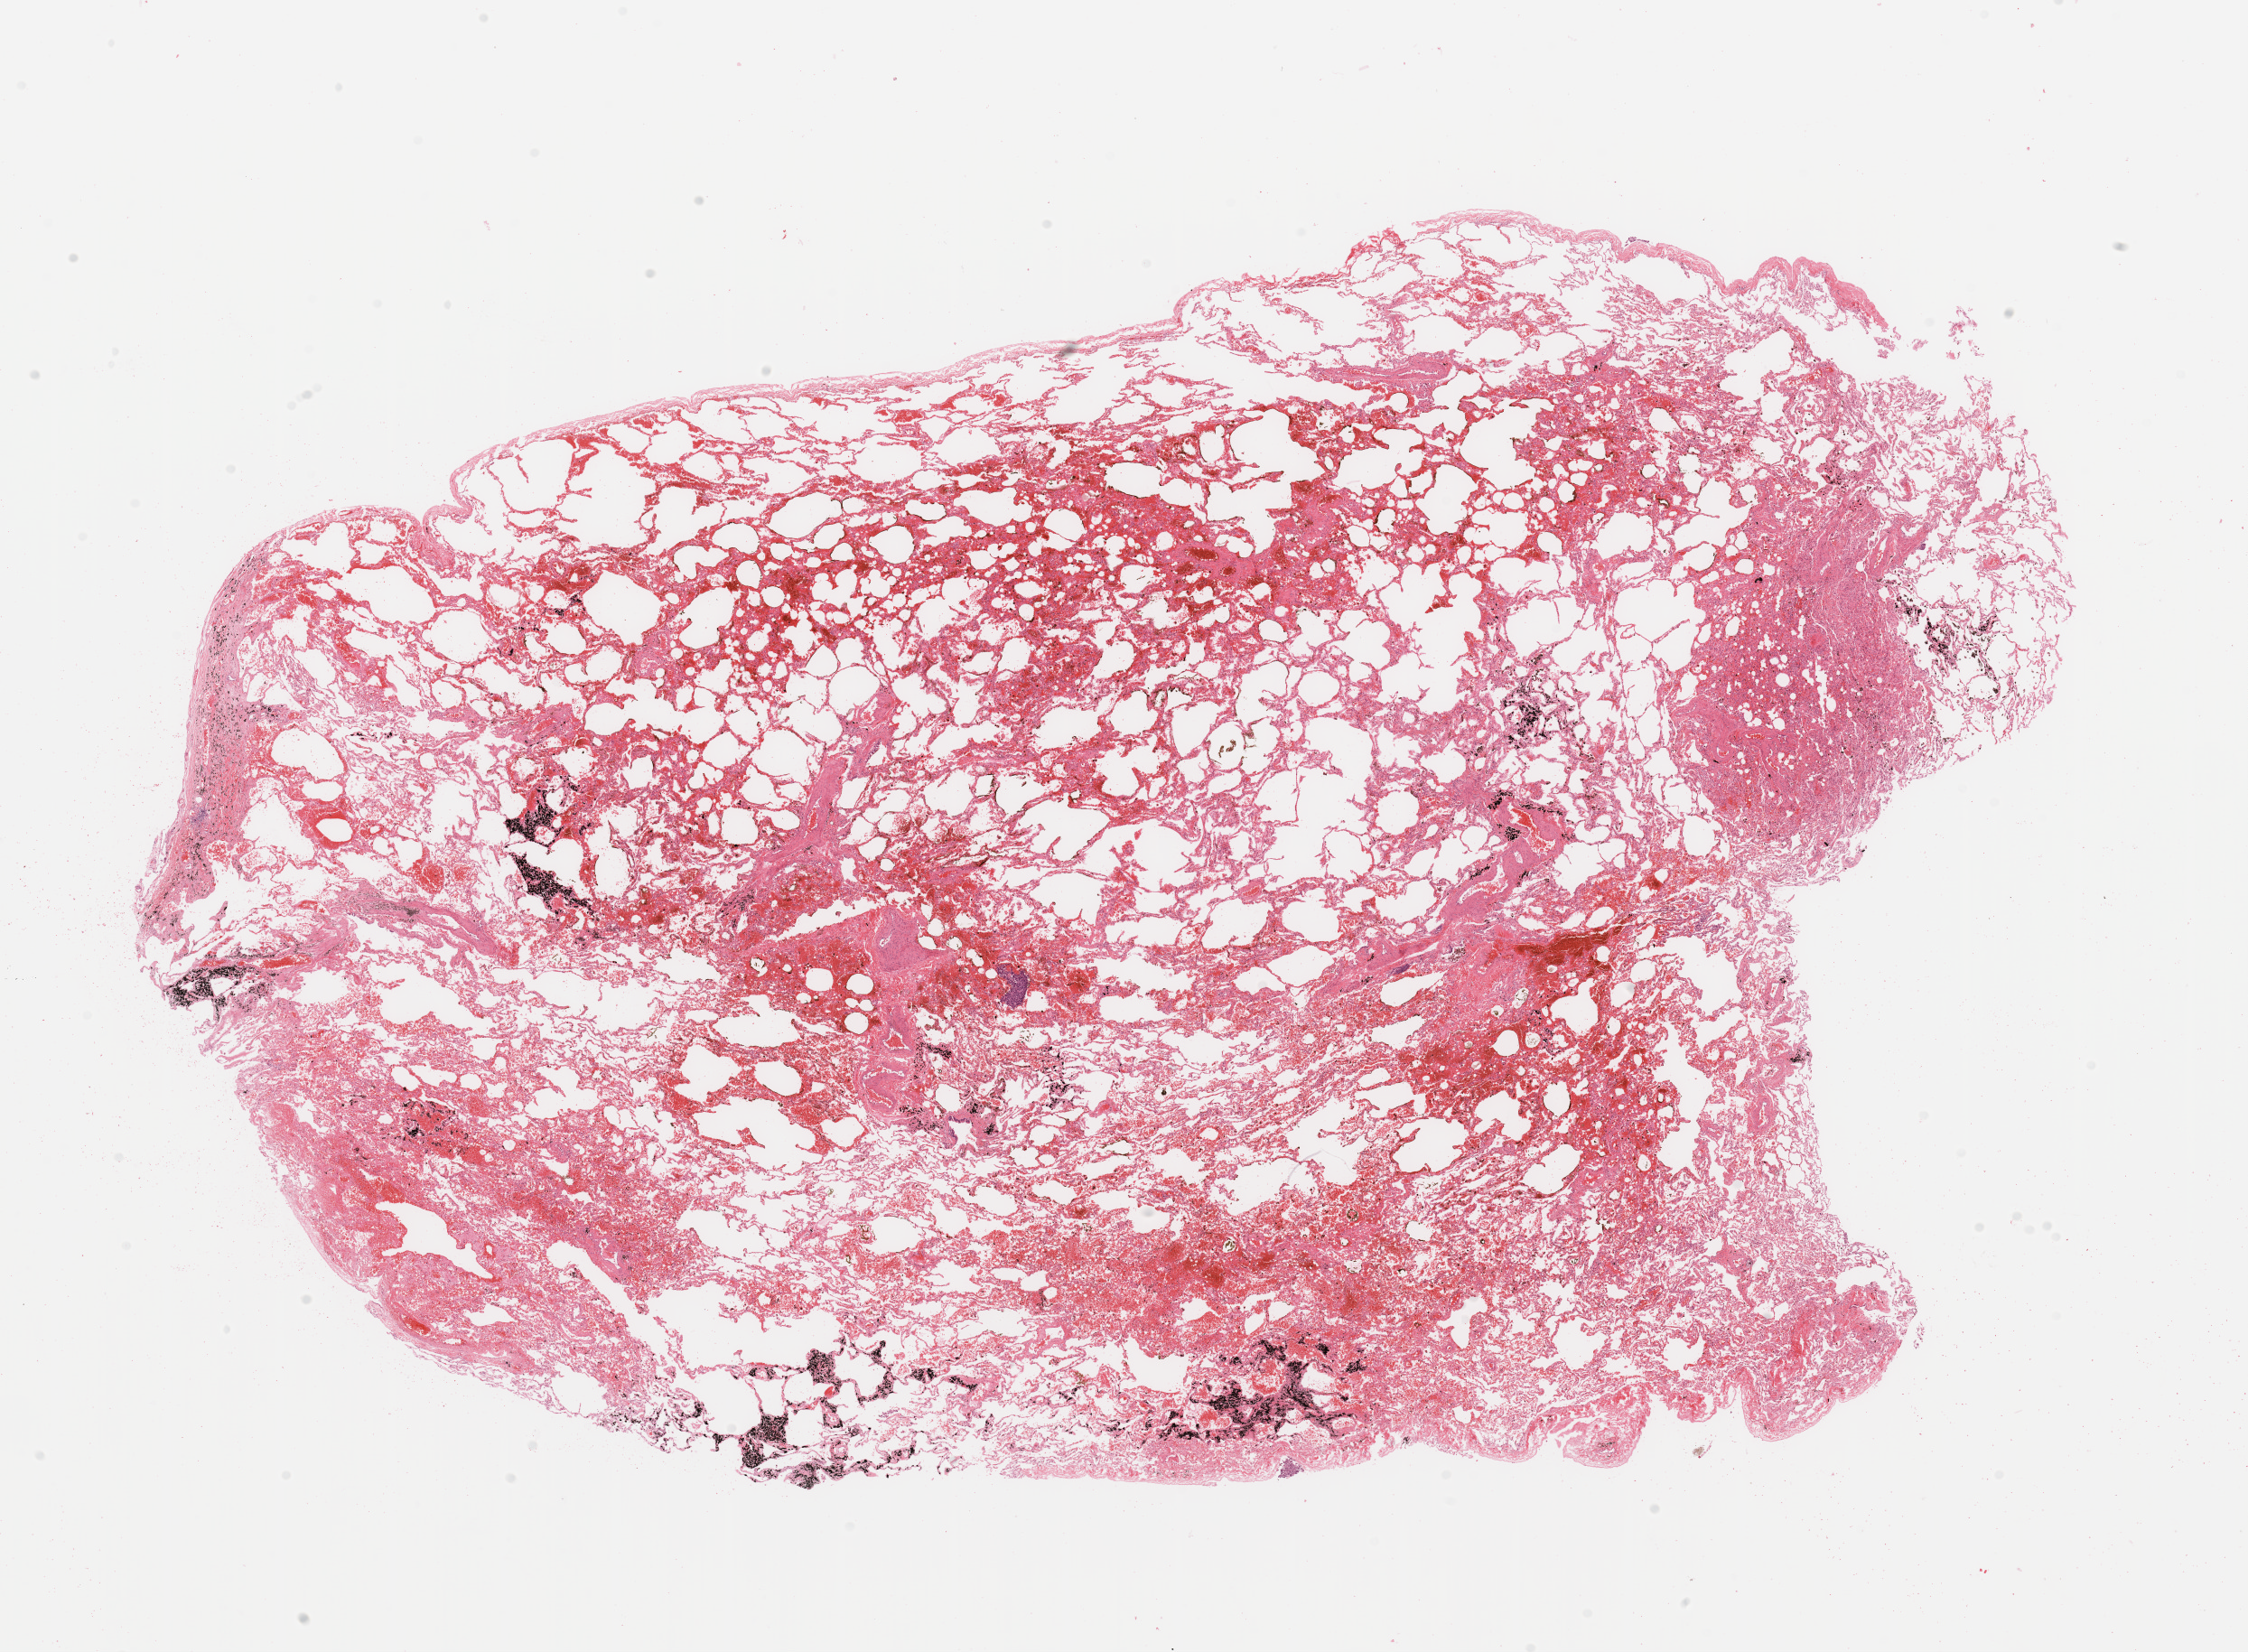
Digitized H&E tissue section (whole slide) — shown as a low-resolution overview of the whole scanned area (about 19.7 x 14.5 mm, slide scanned at 20x); lung, normal (non-tumour) tissue. 56-year-old male patient.
This section: normal (non-tumour) tissue from the same patient. Patient diagnosis: Adenocarcinoma, NOS.